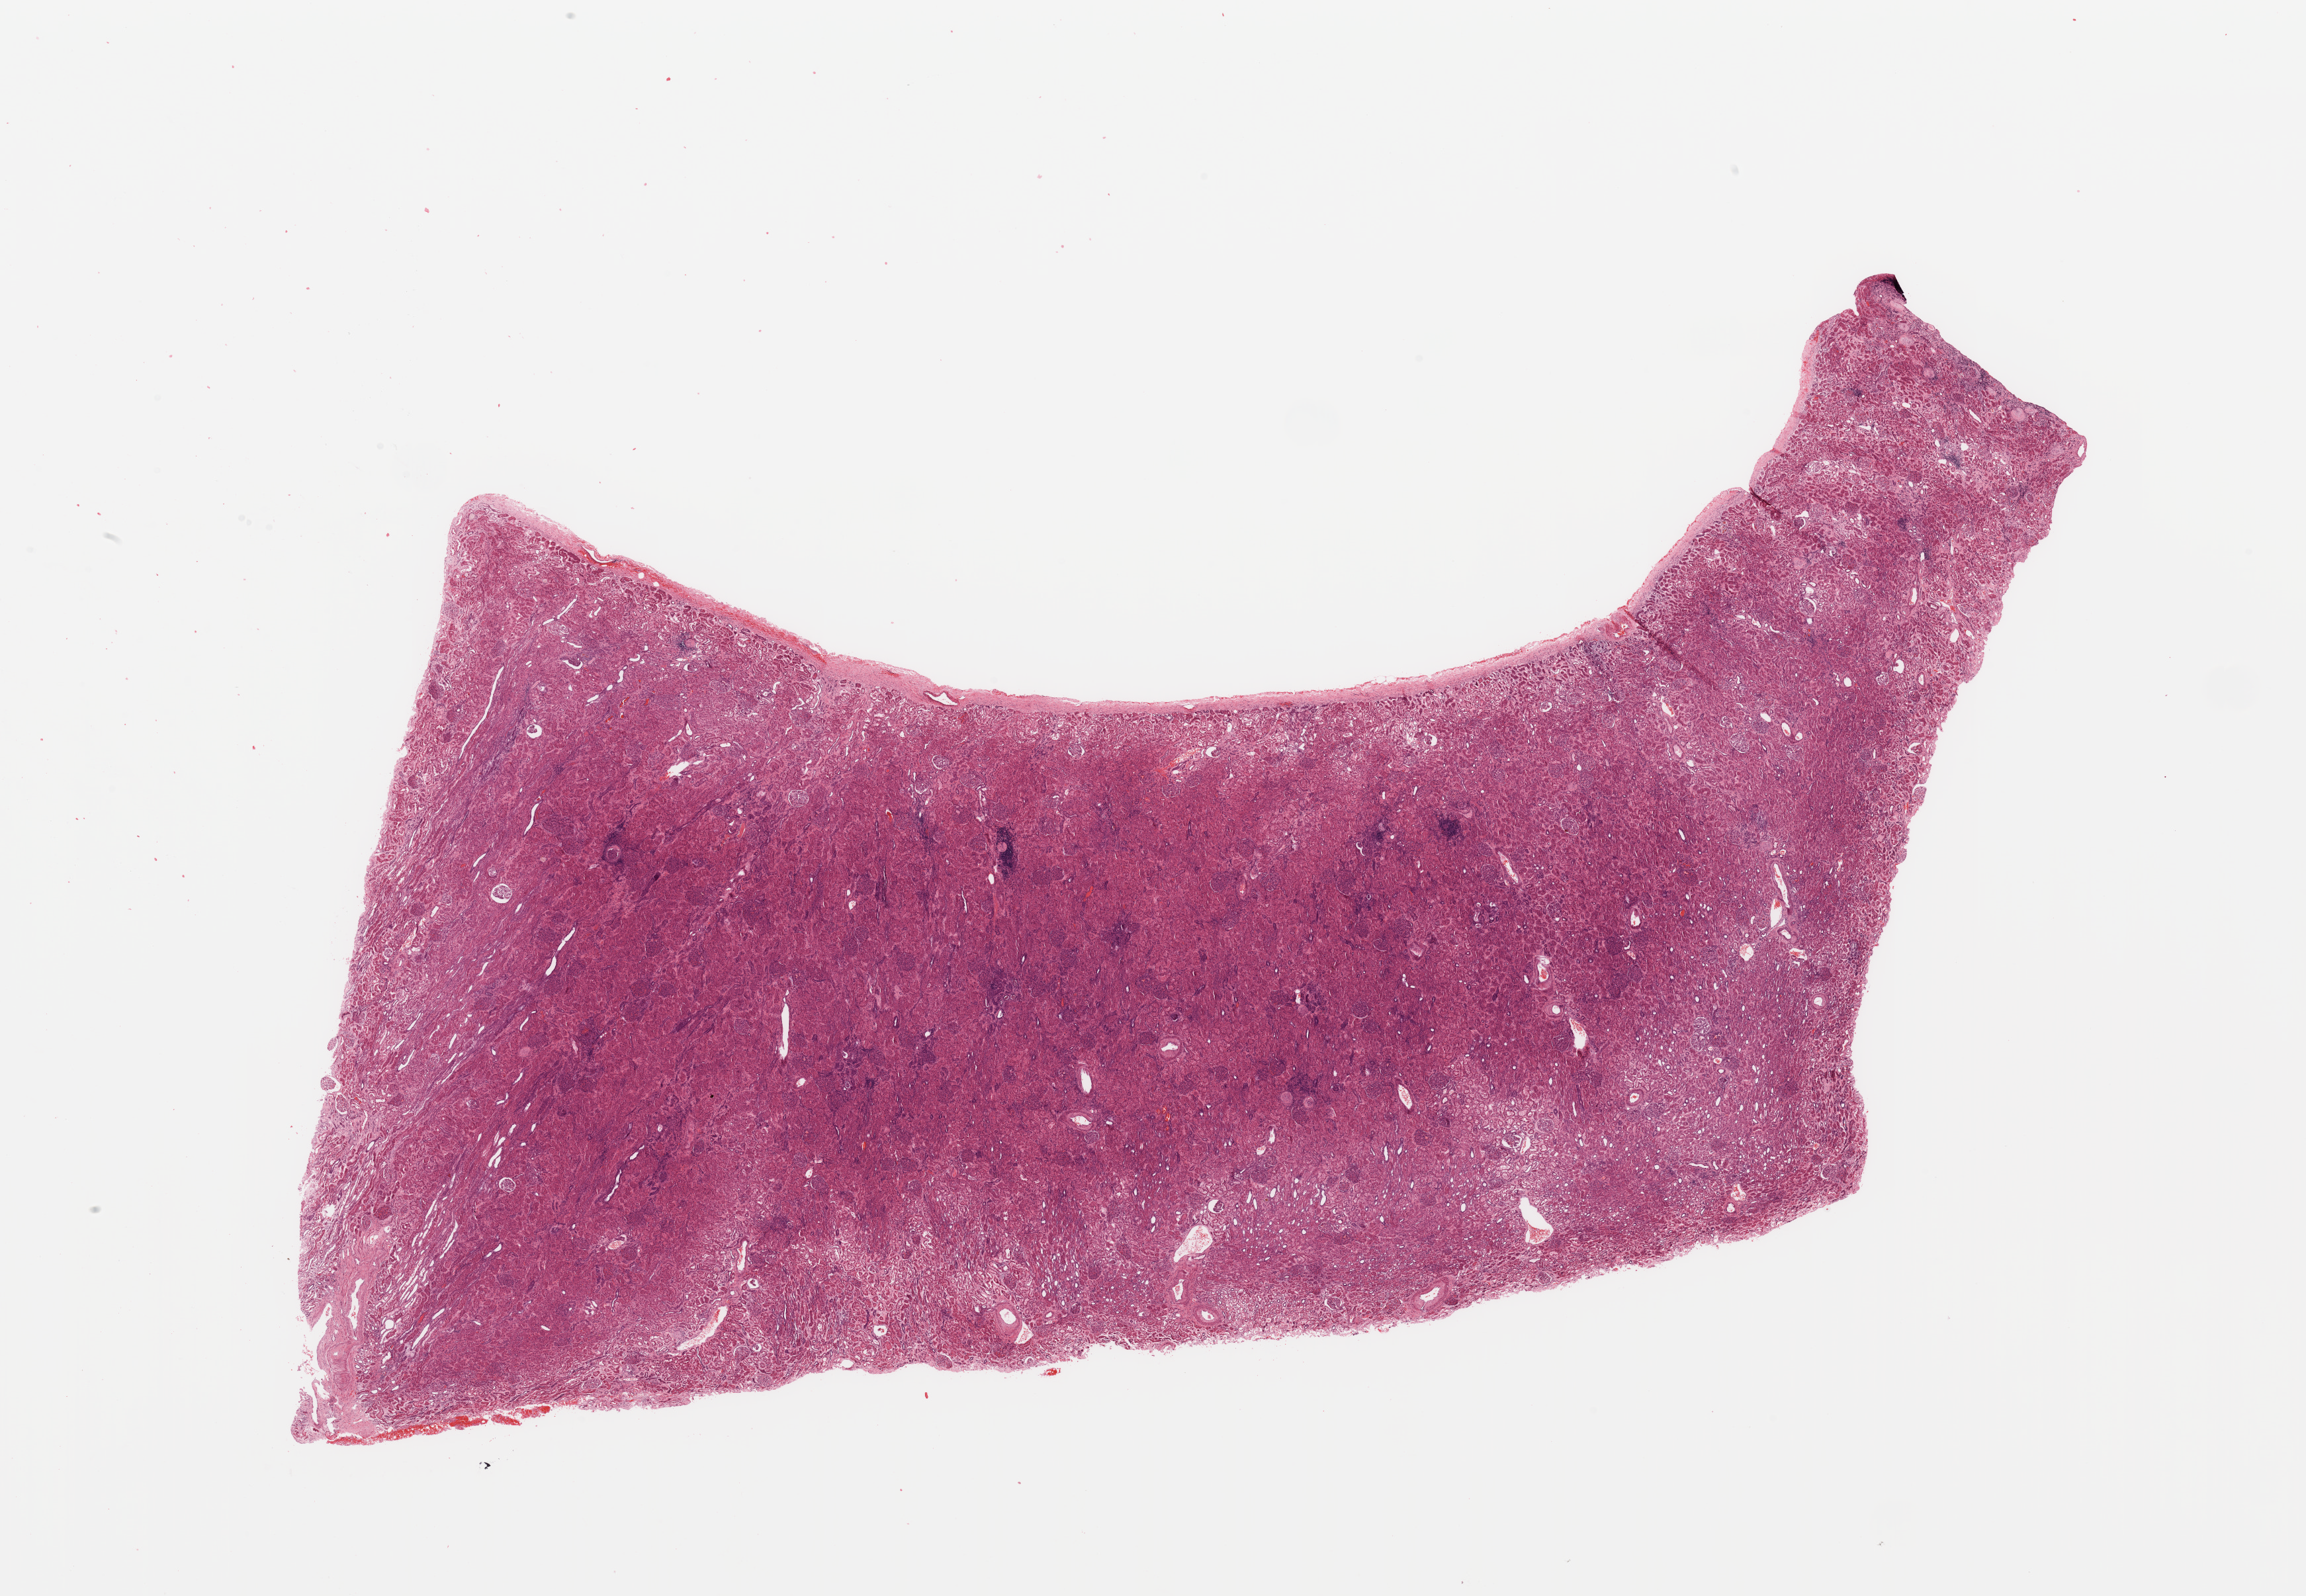
Whole-slide histology image, H&E — whole scanned area (about 27.6 x 19.1 mm, from a 20x scan) shown as a low-resolution overview, normal (non-tumour) tissue sample, sampled site: kidney. Male, 63 y/o.
- this section: normal (non-tumour) tissue from the same patient
- patient diagnosis: Renal cell carcinoma, NOS